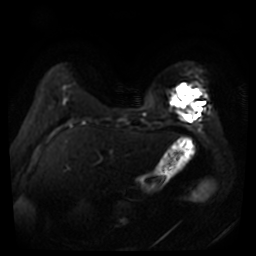
Breast MRI, one axial slice. Slice 11 of 44 in the series (ordered by position). Diffusion-weighted series; image 2 of 4 stored at this slice position (different b-values; order by instance number). 3 T. 256 × 256 image matrix, field of view 360 × 360 mm. Female patient.
Structures marked on this image (manually delineated by an expert):
- tumour on diffusion-weighted imaging: bounding box [x1, y1, x2, y2] px = [172, 92, 201, 112]